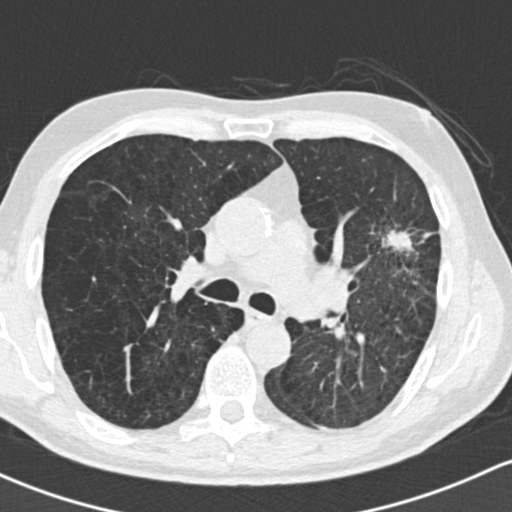
Low-dose screening chest CT, one axial slice; slice 95 of 162 in the series (ordered by position); lung window (W 1500 / L -600 HU); 512 × 512 image matrix, field of view 318 × 318 mm.
Structures marked on this image (outlined manually by an expert reader):
- lesion 1 (tumor, upper lobe of left lung): bounding box (x1, y1, x2, y2) in pixels: (382, 230, 413, 254)